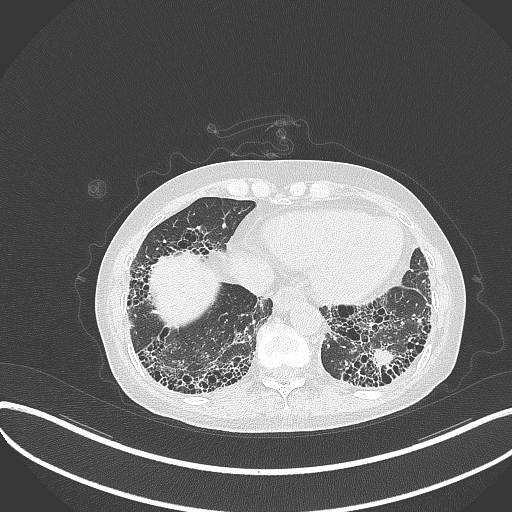
Chest CT, one axial slice; slice 71 of 373 in the series (ordered by position); reconstruction kernel B70f; 120 kVp; lung window (W 1500 / L -600 HU); 1 mm slice thickness; 512 × 512 image matrix, field of view 400 × 400 mm. Female patient, age 56 years. From the clinical record (not read from this slice): clinical TNM (as recorded): T1 N0 M0.
Outlined on this slice (bounding box drawn by a radiologist):
- lung tumour (recorded histology: adenocarcinoma): bounding box <369,345,394,372> (left, top, right, bottom; pixels)